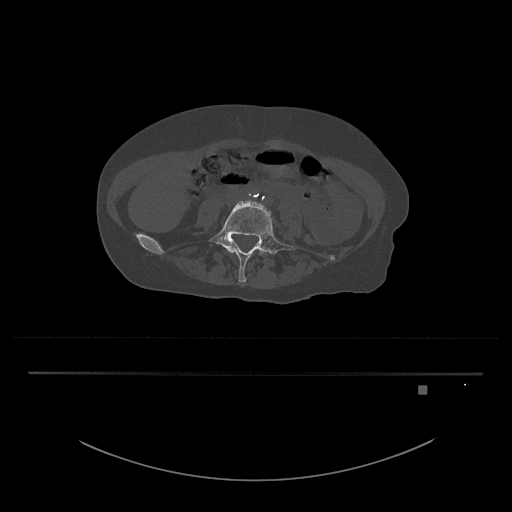
CT including the spine, one axial slice; position 311 of 797 along the scan axis; reconstruction kernel Br40s/3; 120 kVp; bone window (W 1800 / L 400 HU); 0.5 mm slice thickness; 512 × 512 image matrix. Patient: female, 57 years. From the clinical record (not read from this slice): primary cancer: cervical.
Annotated regions visible in this slice (semi-automatically segmented with operator editing):
- L4 vertebra: bounding box (x1, y1, x2, y2) in pixels: (231, 250, 263, 255)